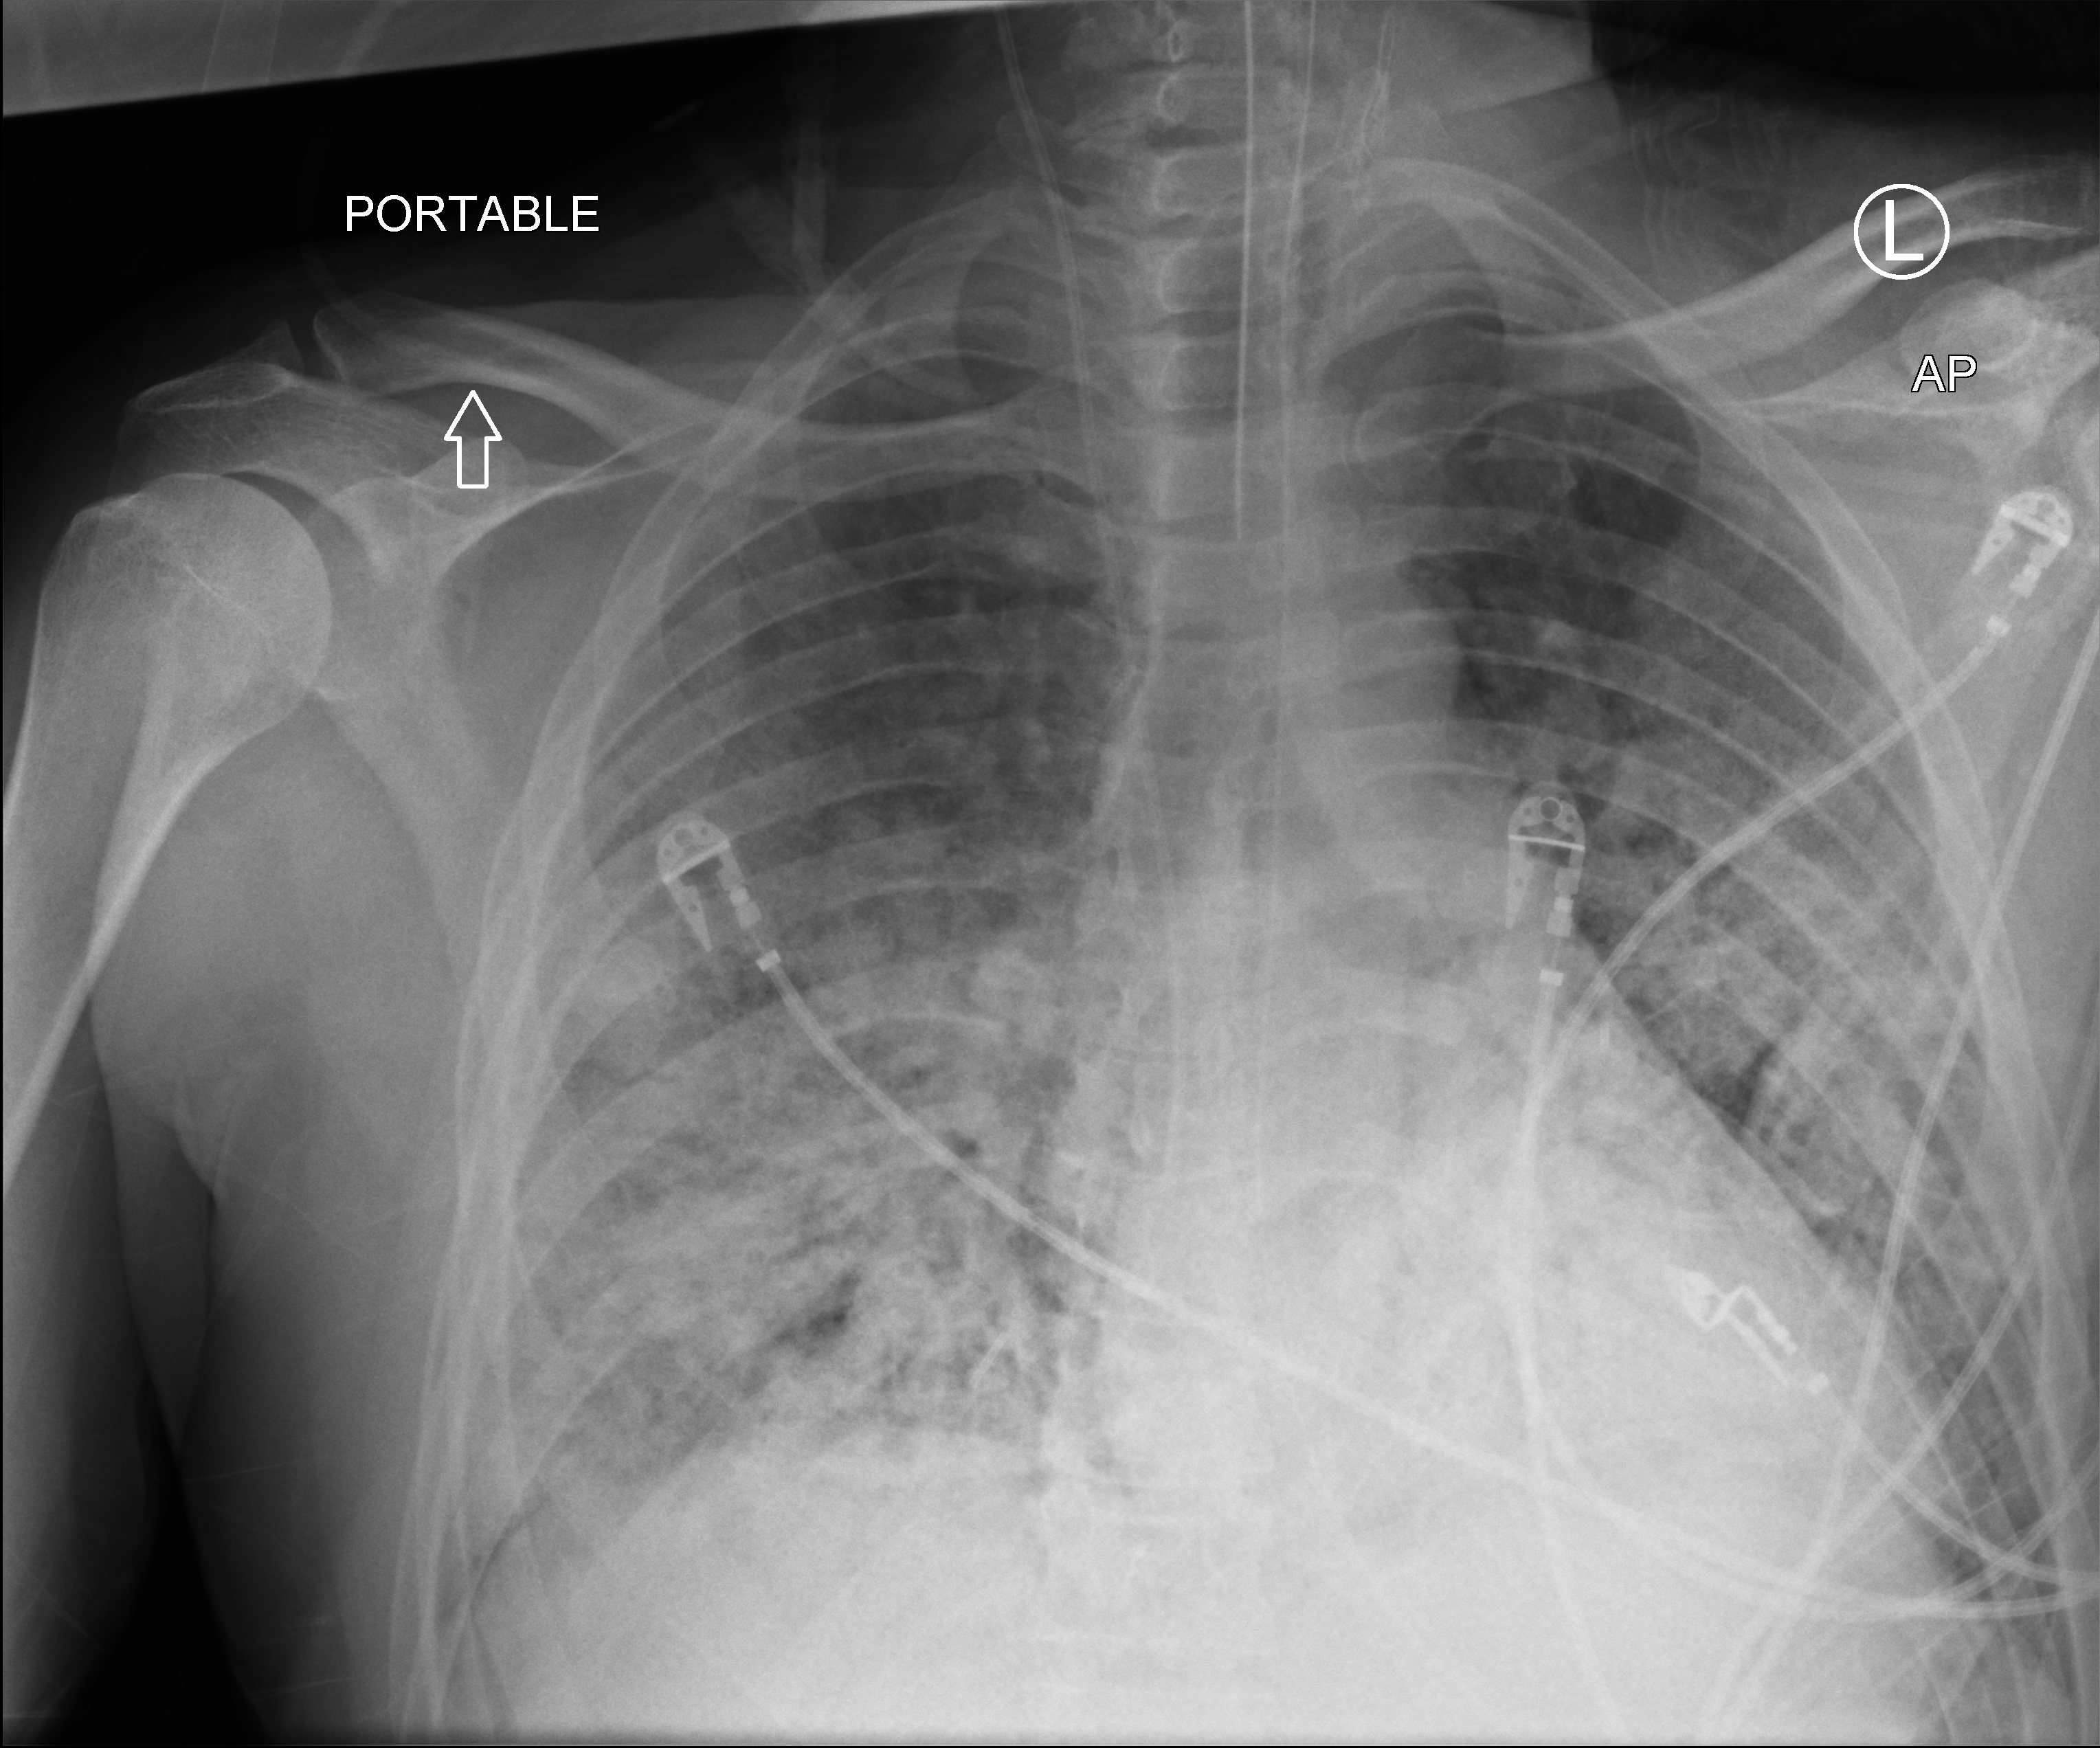
Chest X-ray (portable). Patient hospitalised with COVID-19; male, aged 18–59 years.
From the hospital-stay record, not from the radiograph (when in the stay this image was taken is not recorded):
- other chronic lung disease (admission record): no